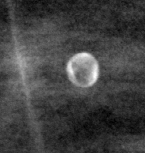
Crop from a digitized film mammogram around one marked abnormality, right breast, MLO view, BI-RADS breast density category 1 (scale 1–4).
Marked abnormality: calcifications, morphology eggshell; BI-RADS assessment category 2; subtlety rating 5 on a 1 (subtle) to 5 (obvious) scale; benign; no additional work-up was recommended (benign without callback).